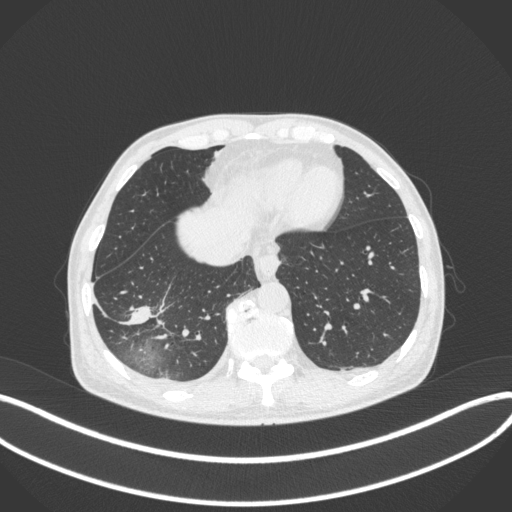
Chest CT, one axial slice; slice 93 of 385 in the series (ordered by position); 120 kVp; lung window (W 1500 / L -600 HU); 1 mm slice thickness; 512 × 512 image matrix. Patient: male, 64 years. From the clinical record (not read from this slice): clinical TNM (as recorded): T3 N0 M0; histopathological grade: G2-3.
Outlined on this slice (bounding box drawn by a radiologist):
- lung tumour (recorded histology: adenocarcinoma): bounding box [x1, y1, x2, y2] px = [123, 303, 155, 332]